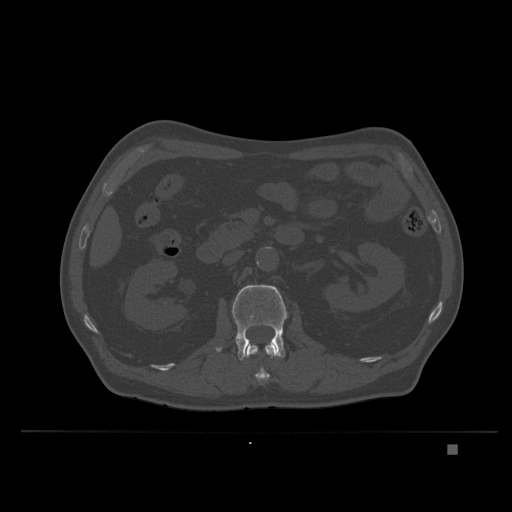
CT including the spine, one axial slice. Position 124 of 435 along the scan axis. Bone window (W 1800 / L 400 HU). 1.5 mm slice thickness. 512 × 512 image matrix. Male patient, age 73 years. From the clinical record (not read from this slice): primary cancer: skin.
Structures marked on this image (semi-automatically segmented with operator editing):
- L1 vertebra: bounding box (x1, y1, x2, y2) in pixels: (245, 340, 277, 385)
- L2 vertebra: (215, 284, 288, 361)